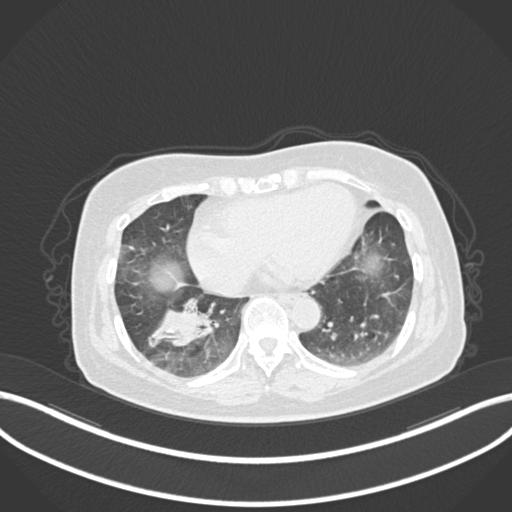
Chest CT, one axial slice. Slice 40 of 222 in the series (ordered by position). 120 kVp. Lung window (W 1500 / L -600 HU). 1 mm slice thickness. 512 × 512 image matrix, field of view 400 × 400 mm. Female patient, age 67 years. Case-level facts recorded for this patient, not image findings: clinical TNM (as recorded): T1c N1 M0.
Structures marked on this image (rectangle marked by the reading radiologist):
- lung tumour (recorded histology: adenocarcinoma): bounding box (x1, y1, x2, y2) in pixels: (147, 289, 224, 358)